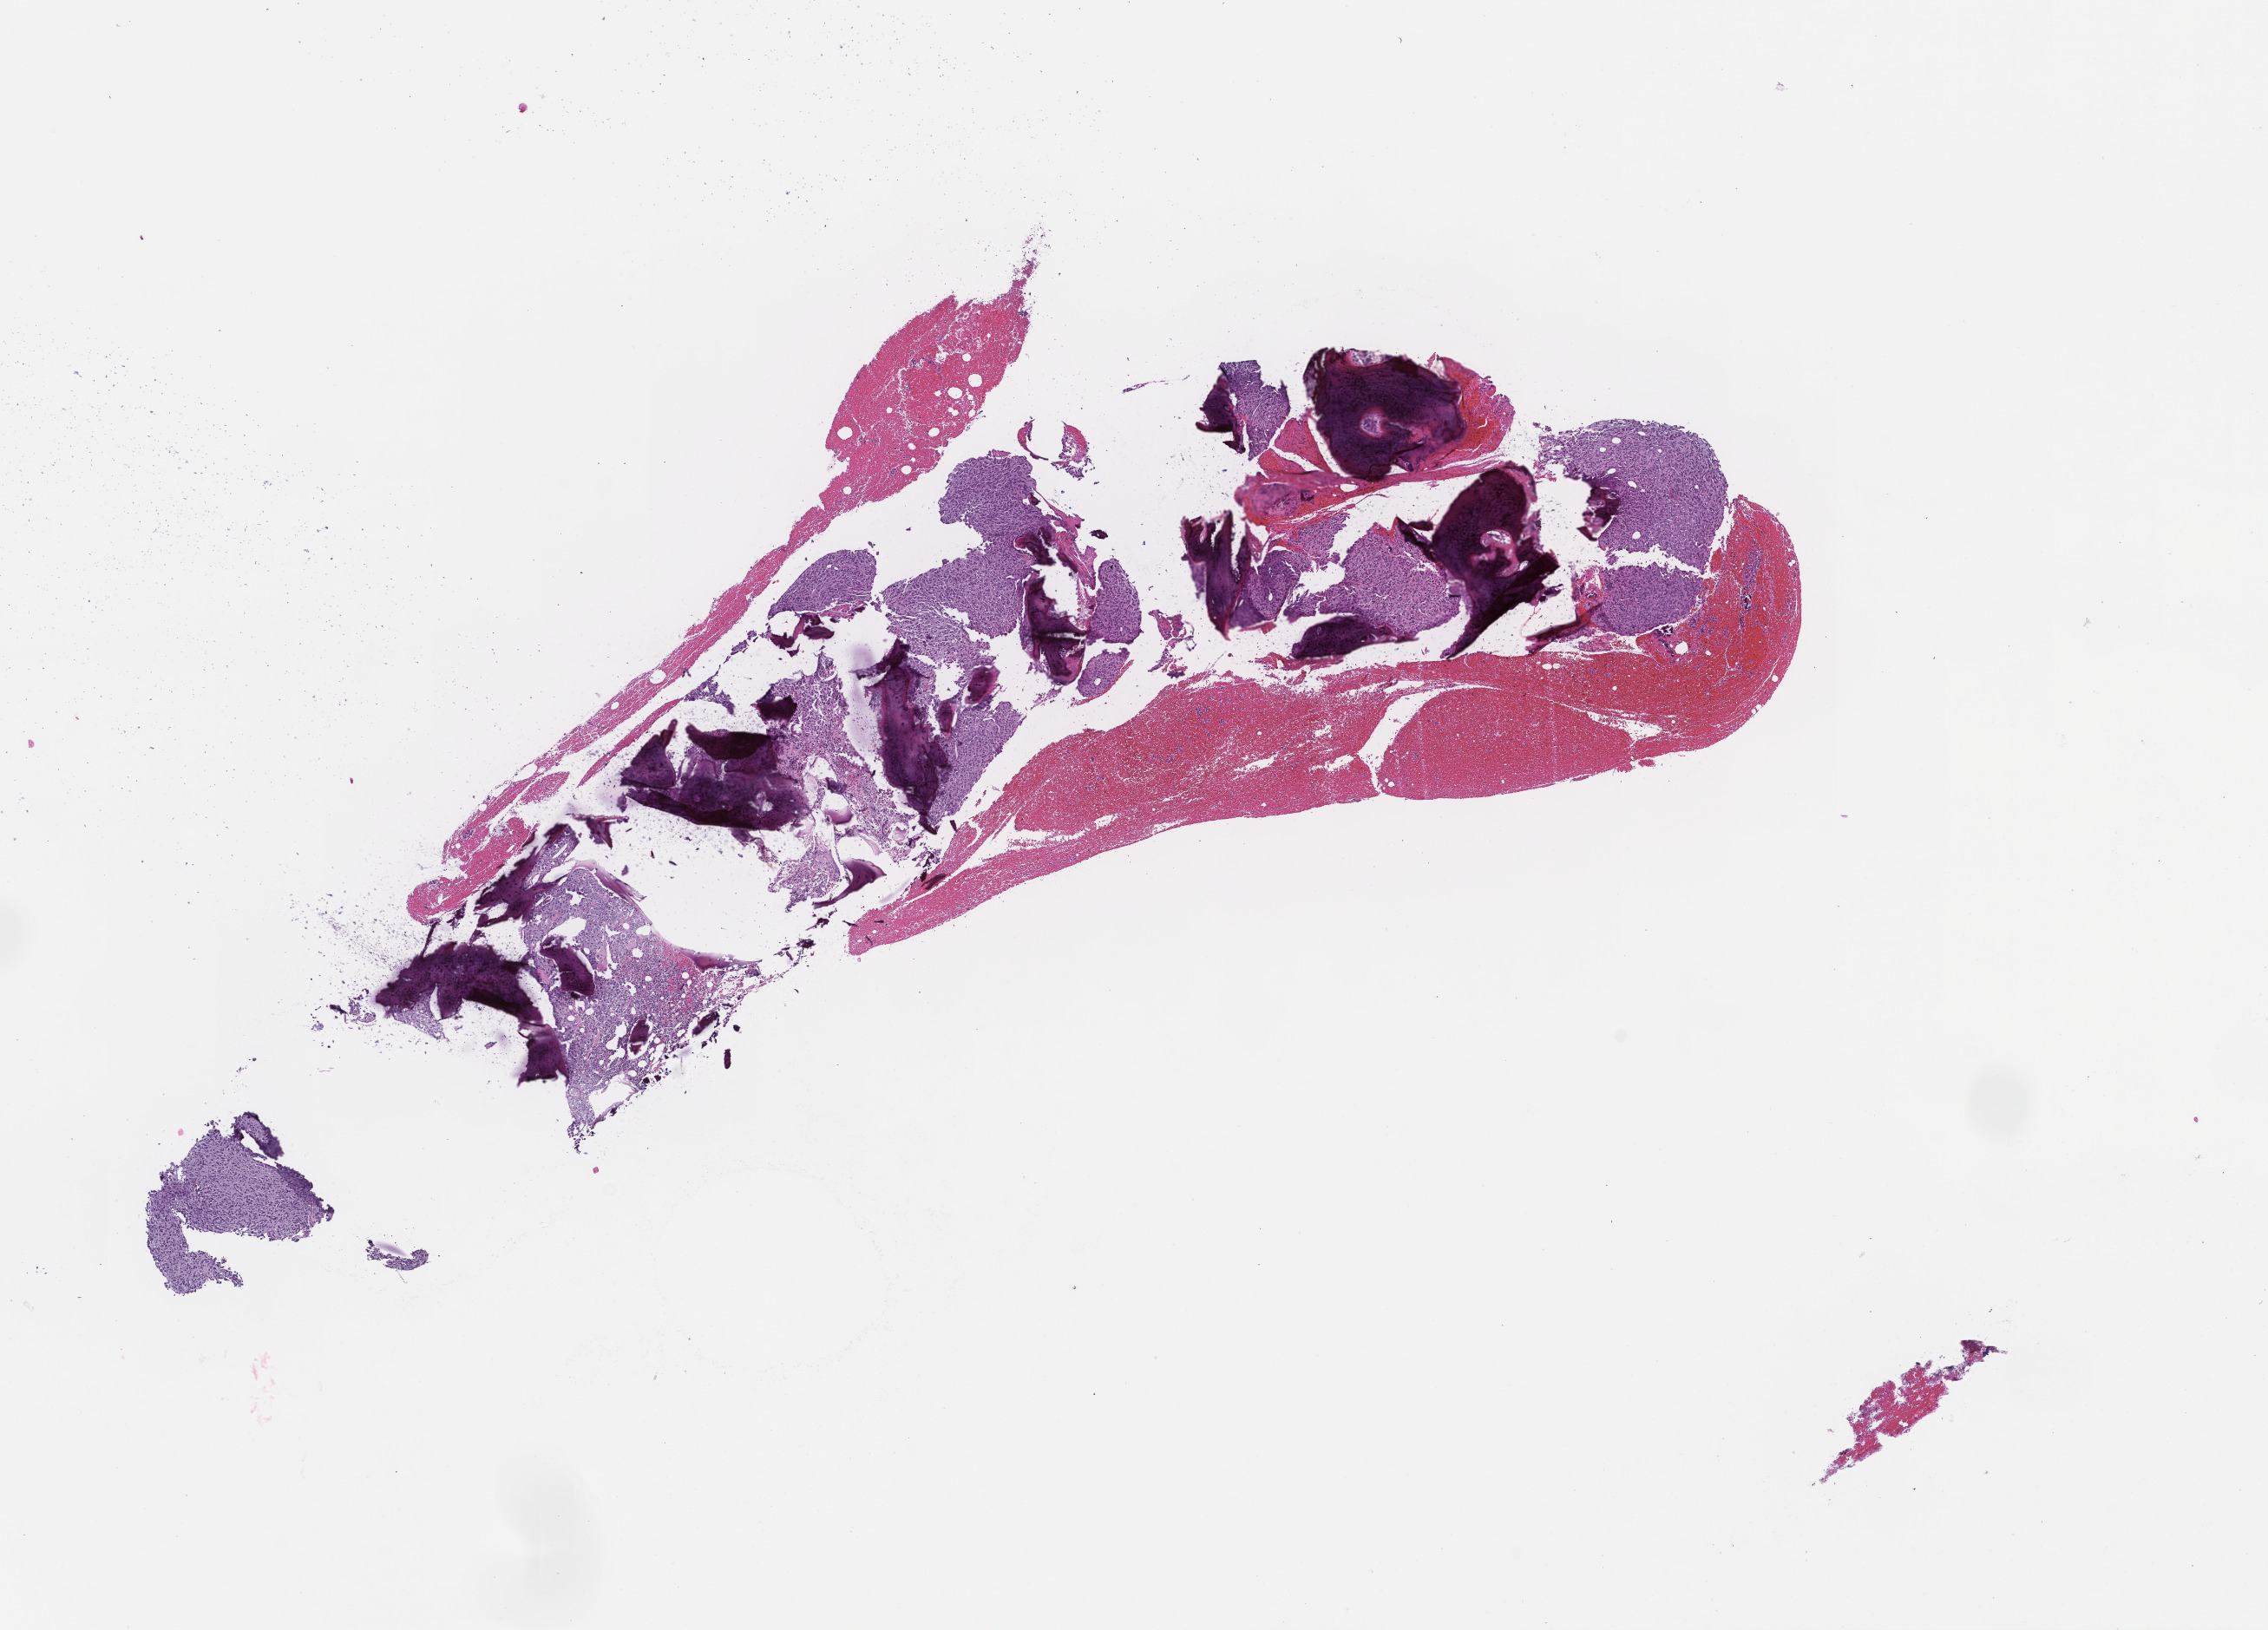
H&E whole-slide image, whole scanned area (about 10.6 x 7.6 mm) shown as a low-resolution overview. Formalin-fixed, paraffin-embedded (FFPE) tissue. Specimen time point: archival tissue. Patient: female.
• this section: metastasis (sampled organ not recorded)
• primary diagnosis of the patient: Invasive Breast Carcinoma